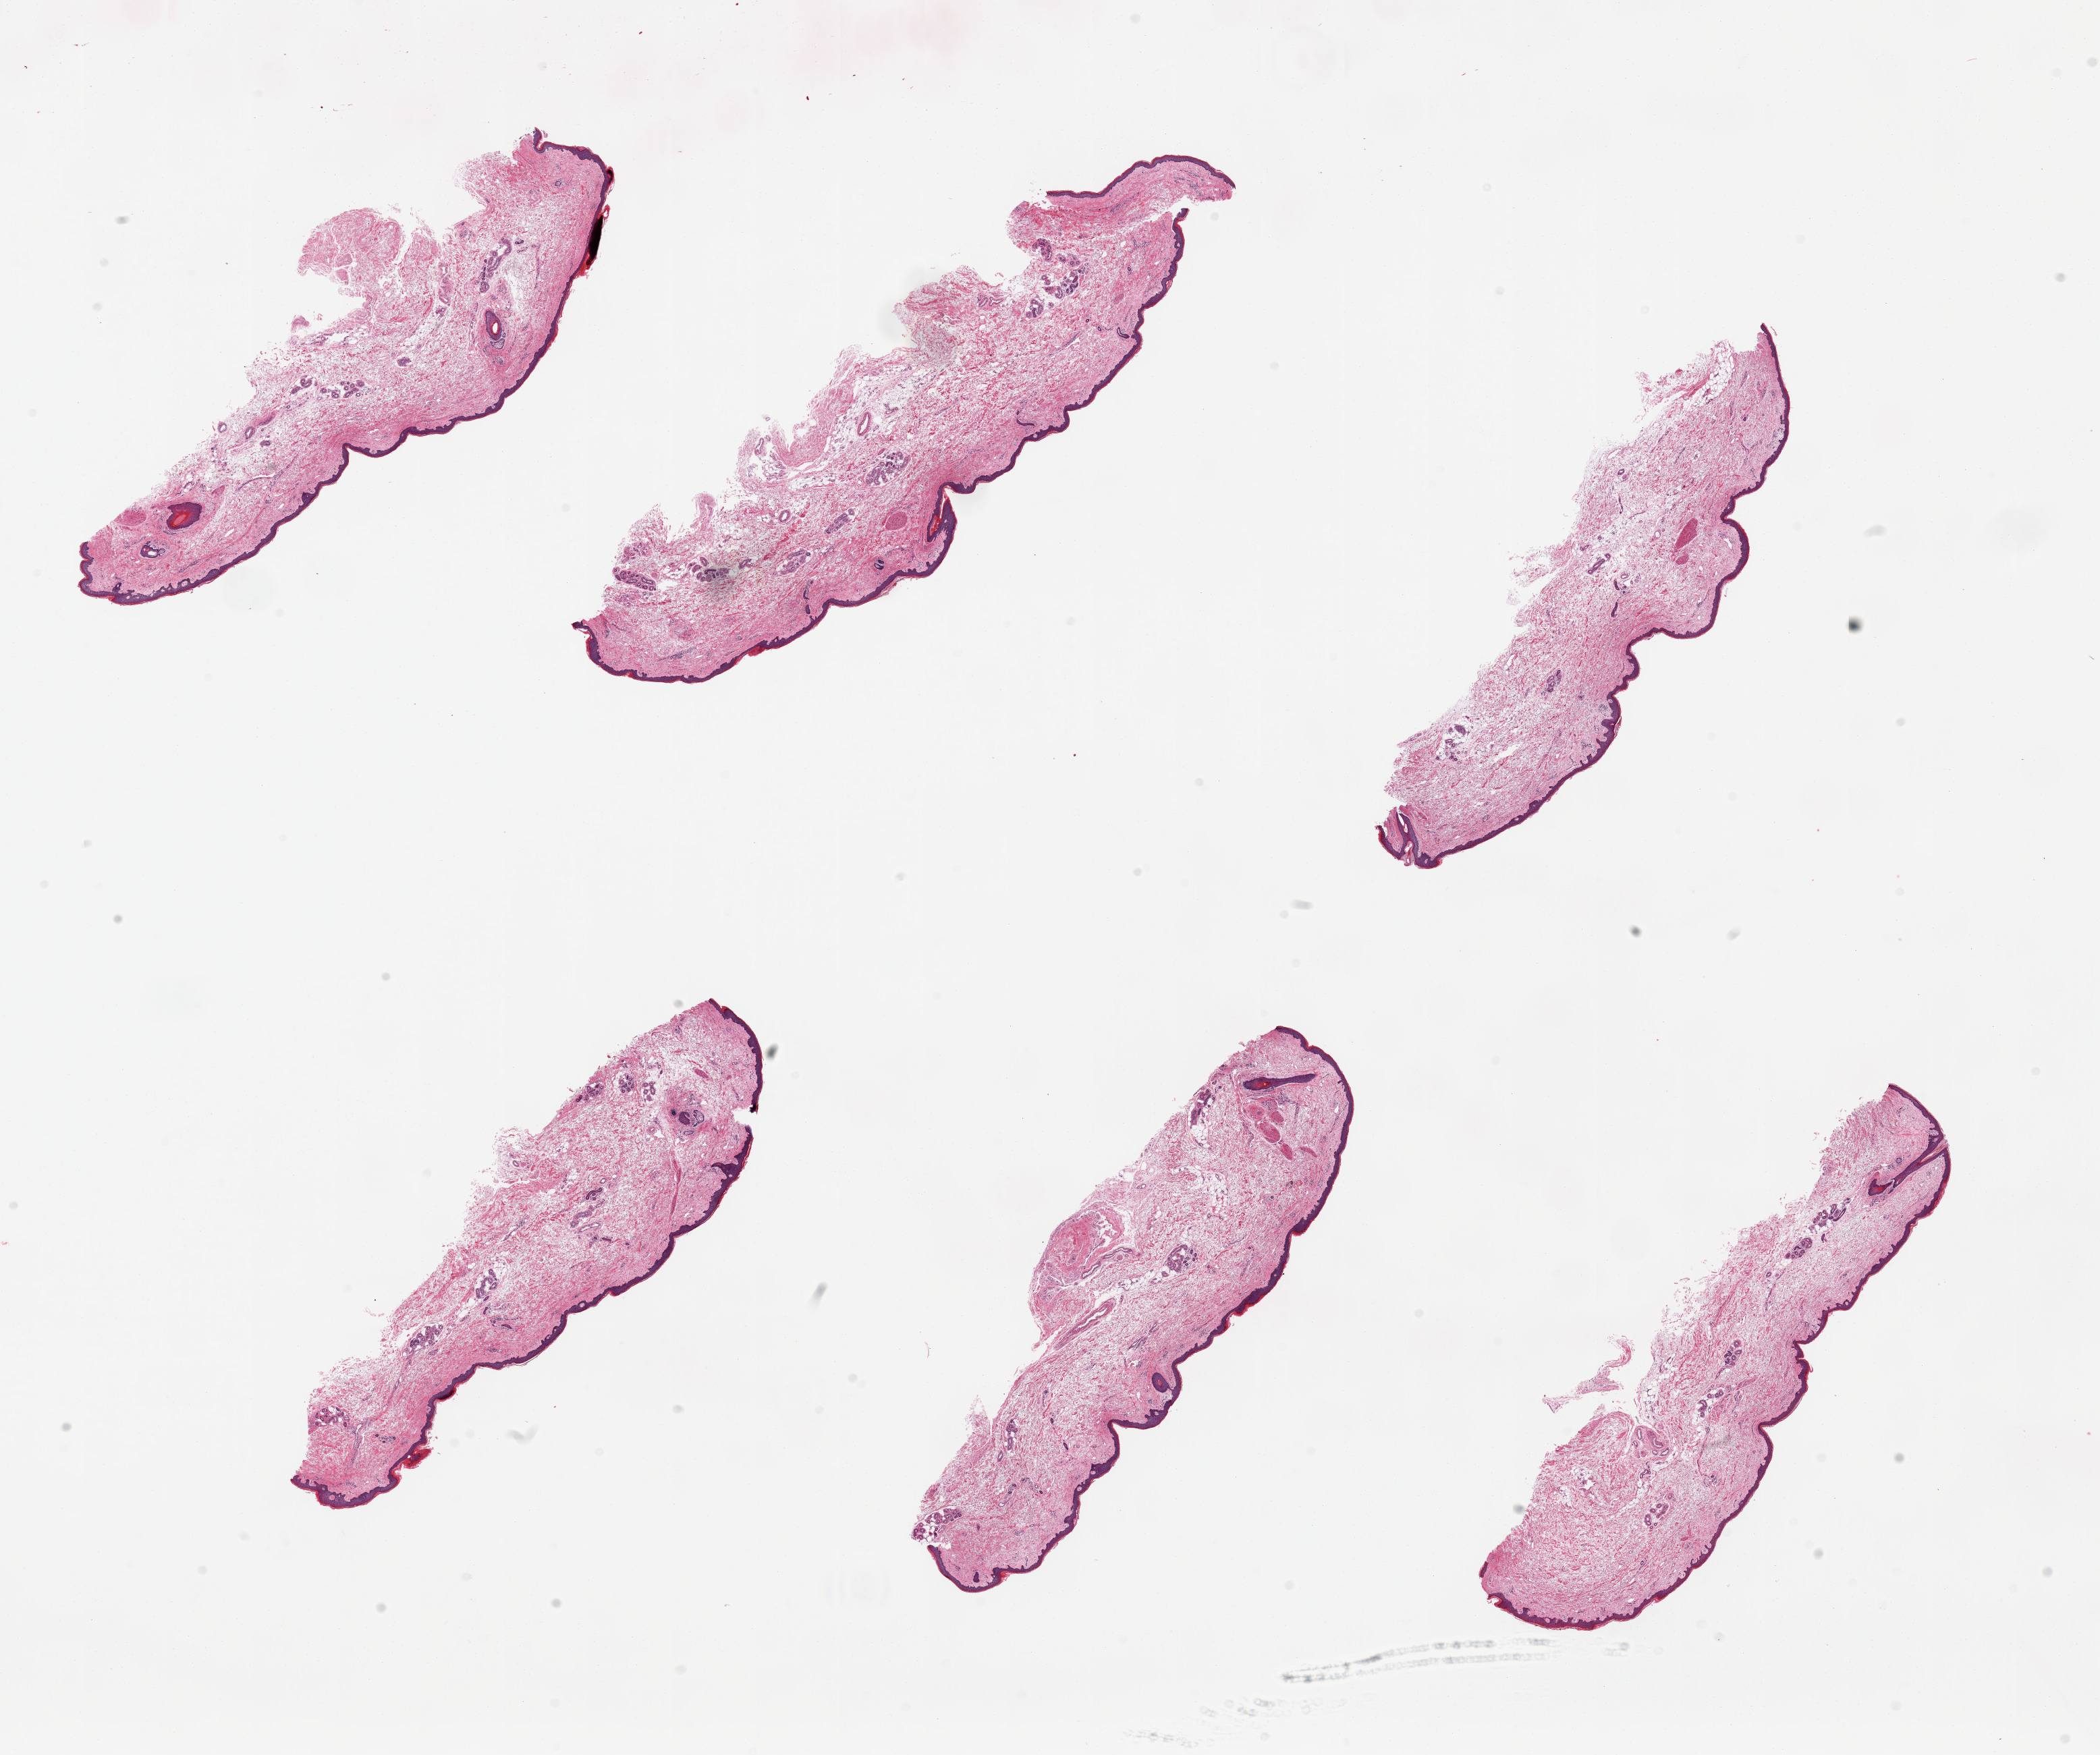
Digitized haematoxylin and eosin-stained section — whole scanned area (about 24.6 x 20.6 mm) shown as a low-resolution overview. PAXgene-fixed, paraffin-embedded tissue. Sampled site (target tissue): skin of lower leg. Donor tissue sample. Male donor.
• pathologist's review note for this sample: 6 pieces, no dermal fat, squamous epithelium is ~40-50 microns